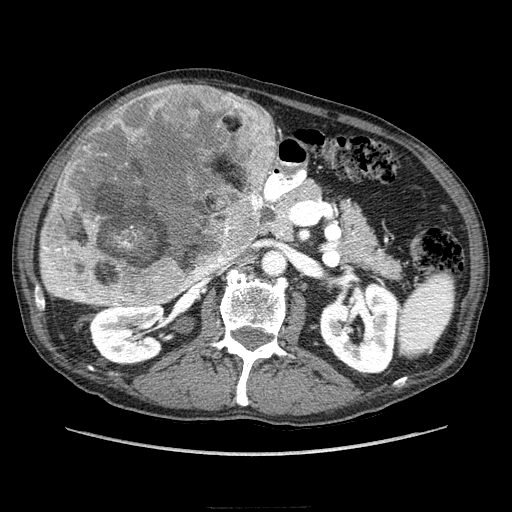
Contrast-enhanced abdominal CT (liver protocol), one axial slice; slice 113 of 218 in the series (ordered by position); 100 kVp; soft-tissue window (W 400 / L 40 HU); 2.5 mm slice thickness; 512 × 512 image matrix, field of view 380 × 380 mm. Case-level facts recorded for this patient, not image findings: diagnosis: hepatocellular carcinoma (patient treated with transarterial chemoembolisation; whether this scan precedes or follows treatment is not stated here); TNM stage (as recorded): Stage-IIIA; Child-Pugh class: A; tumour differentiation: well differentiated; tumour size: 20 cm.
Structures marked on this image (semi-automatically segmented with operator editing):
- liver parenchyma outside the tumour (the mass and vessels are separate outlines, so this box may not span the whole liver): bounding box [x1, y1, x2, y2] px = [40, 129, 276, 304]
- mass: [44, 82, 276, 308]
- liver vessels: [48, 271, 85, 300]